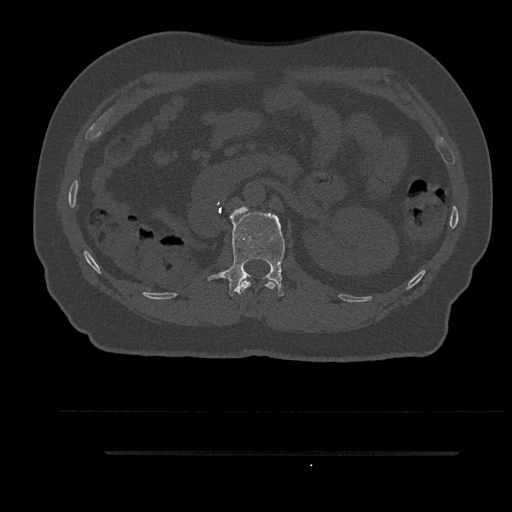
CT including the spine, one axial slice; slice 186 of 797 in the series (ordered by position); 120 kVp; bone window (W 1800 / L 400 HU); 0.5 mm slice thickness; 512 × 512 image matrix. Patient: male, 63 years. Case-level facts recorded for this patient, not image findings: primary cancer: renal; vertebrae with lytic lesions (as recorded): T8.
Outlined on this slice (semi-automatically segmented with operator editing):
- L1 vertebra: box from (x=208, y=207) to (x=285, y=296) px
- T12 vertebra: (x=240, y=280)–(x=277, y=292)